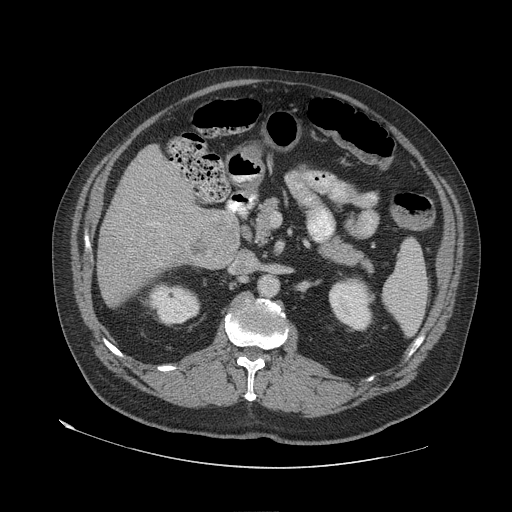
Contrast-enhanced abdominal CT (liver protocol), one axial slice. Slice 25 of 79 in the series (ordered by position). 140 kVp. Soft-tissue window (W 400 / L 40 HU). 2.5 mm slice thickness. 512 × 512 image matrix, field of view 480 × 480 mm. Case-level facts recorded for this patient, not image findings: diagnosis: hepatocellular carcinoma (patient treated with transarterial chemoembolisation; whether this scan precedes or follows treatment is not stated here); TNM stage (as recorded): Stage-IVA; Child-Pugh class: A; tumour differentiation: well differentiated; tumour nodularity: multinodular.
Annotated regions visible in this slice (semi-automatically segmented with operator editing):
- liver parenchyma outside the tumour (the mass and vessels are separate outlines, so this box may not span the whole liver): bounding box <96,145,238,304> (left, top, right, bottom; pixels)
- liver vessels: <158,223,160,225>